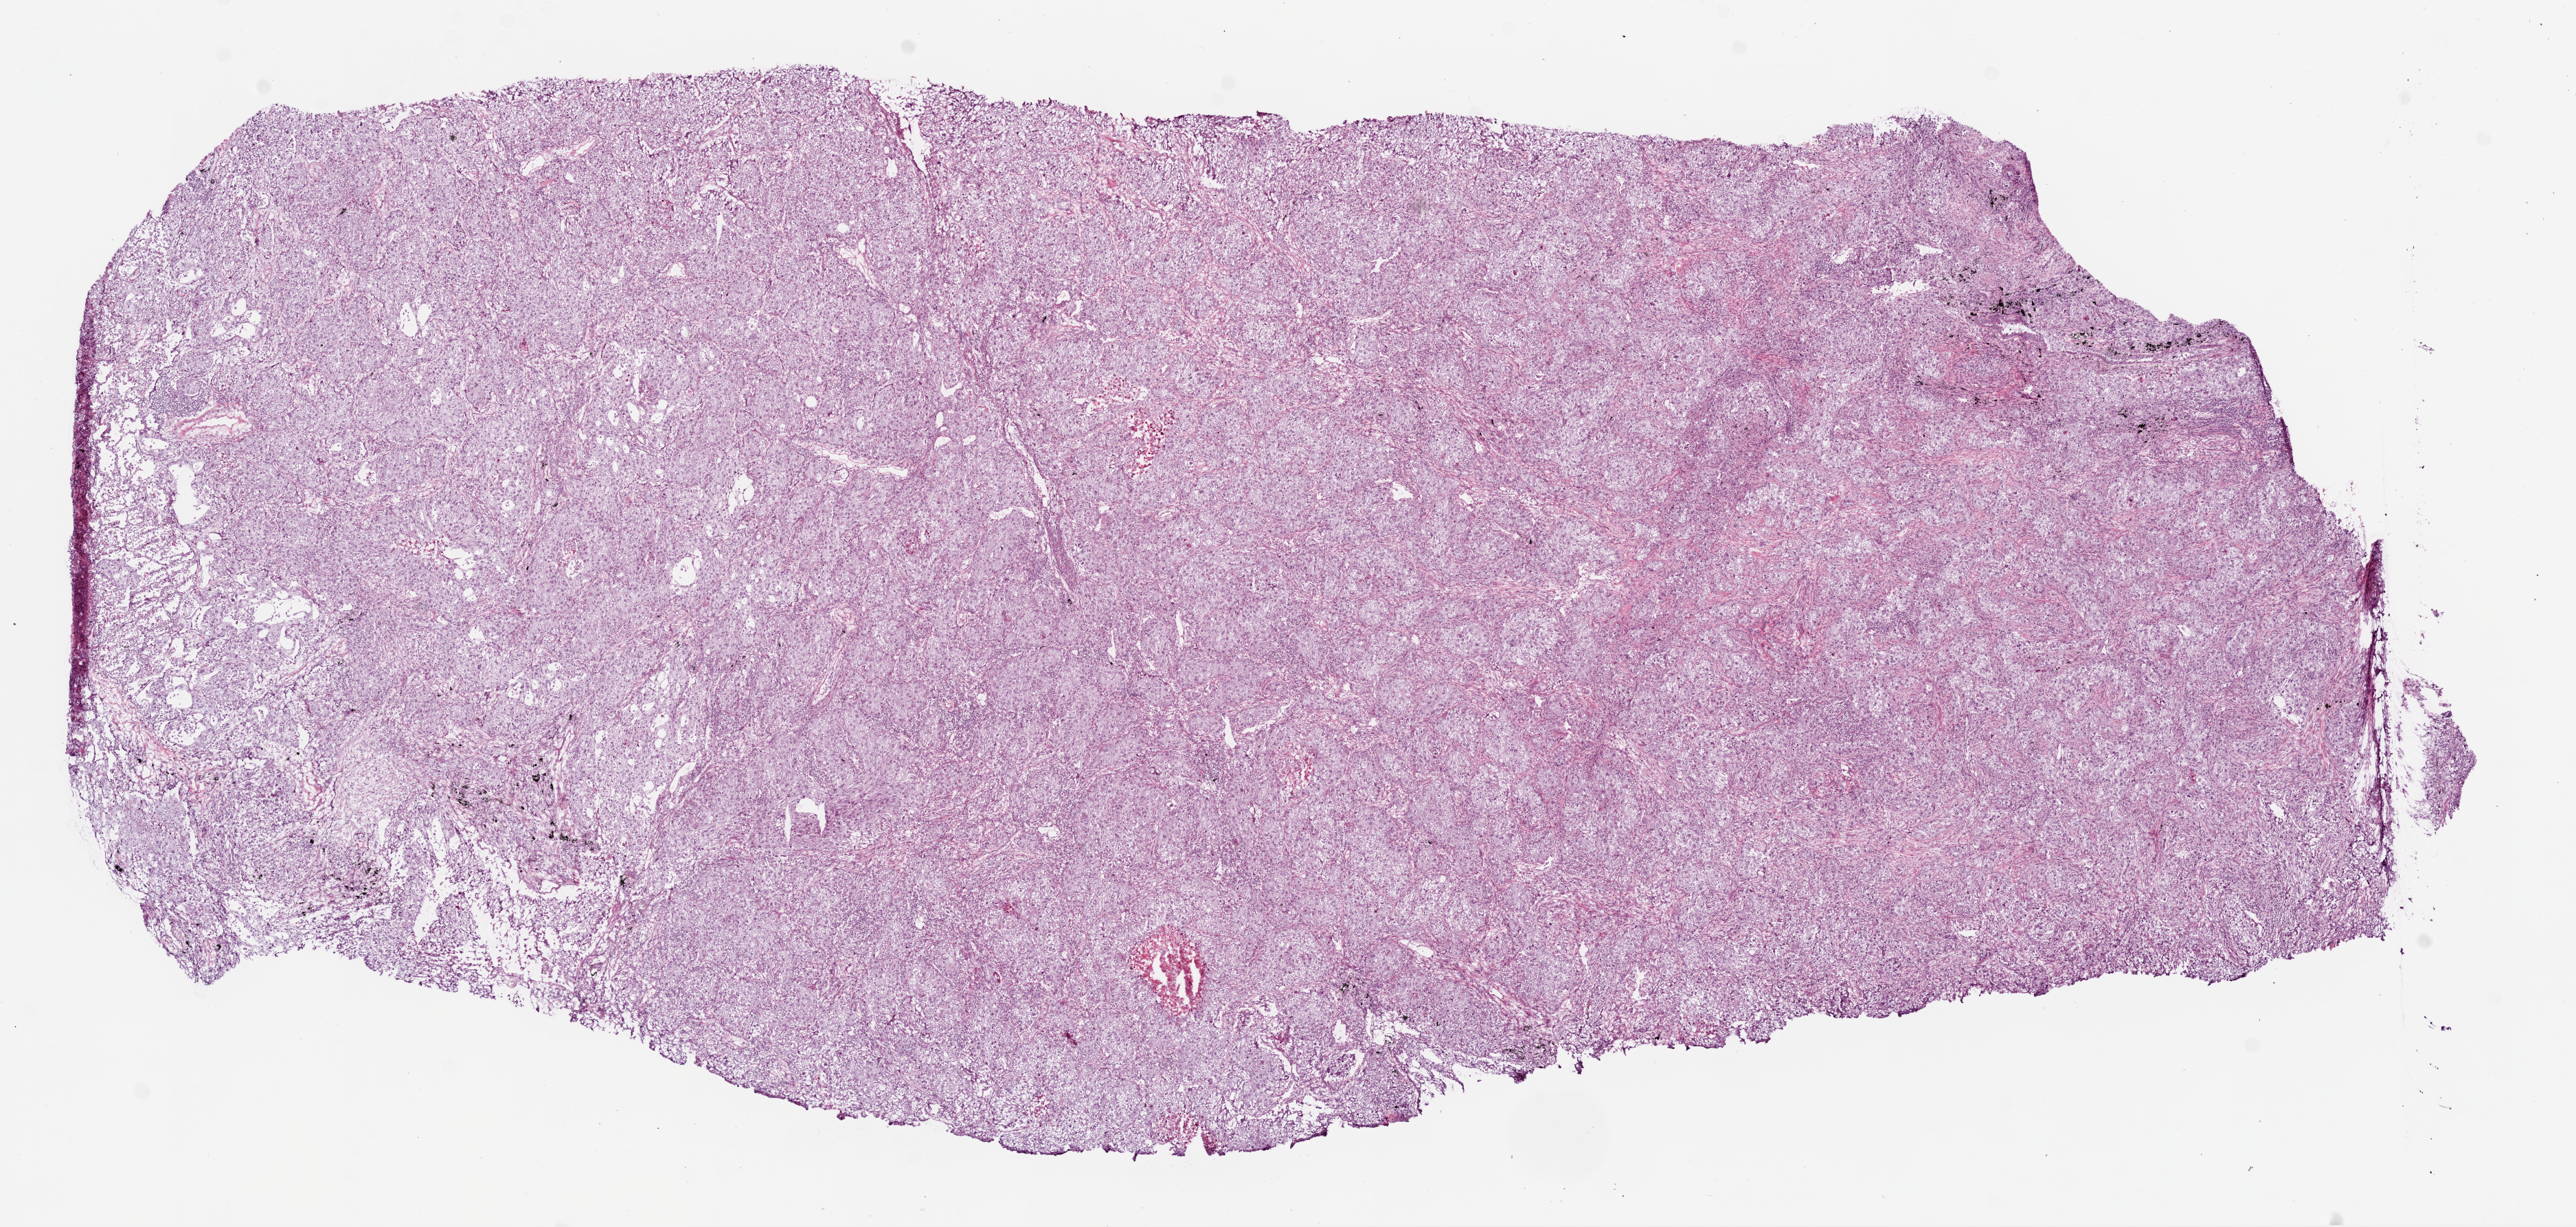
Digitized H&E tissue section (whole slide), a low-resolution overview of the entire scanned area, about 15.0 x 7.2 mm (acquisition: 20x scan). Frozen section from the bottom of the tissue portion. Sample: primary tumour, lung. Male patient. Composition of this section per pathologist review: tumour cells 90%, tumour nuclei 80%, normal cells 0%, stromal cells 5%, necrosis 5%.
Diagnosis: Adenocarcinoma, NOS (upper lobe, lung). AJCC pathologic stage: IIB. TNM: T2 N1 M0.